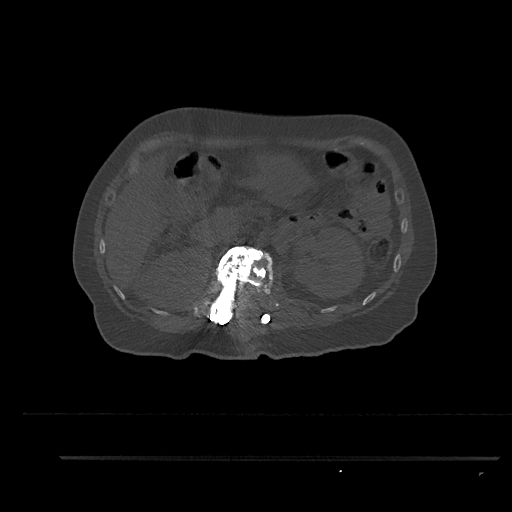
CT including the spine, one axial slice. Slice 219 of 797 in the series (ordered by position). Reconstruction kernel Br40s/3. 120 kVp. Bone window (W 1800 / L 400 HU). 0.5 mm slice thickness. 512 × 512 image matrix, field of view 408 × 408 mm. Female patient, age 44 years. Case-level facts recorded for this patient, not image findings: primary cancer: renal; vertebrae with lytic lesions (as recorded): L1.
Annotated regions visible in this slice (semi-automatic segmentation, software-assisted and operator-edited):
- L1 vertebra: bounding box <207,246,275,324> (left, top, right, bottom; pixels)